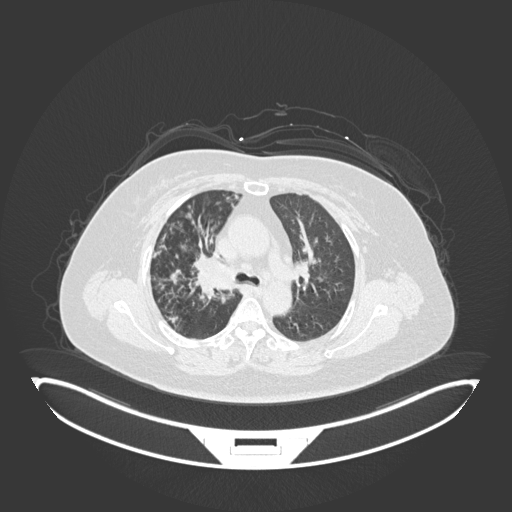
Chest CT, one axial slice; position 120 of 245 along the scan axis; 120 kVp; lung window (W 1500 / L -600 HU); 512 × 512 image matrix. Female patient, age 60 years. Case-level facts recorded for this patient, not image findings: clinical TNM (as recorded): T1c N0 M0.
Outlined on this slice (bounding box drawn by a radiologist):
- lung tumour (recorded histology: squamous cell carcinoma): bounding box [x1, y1, x2, y2] px = [197, 253, 239, 293]